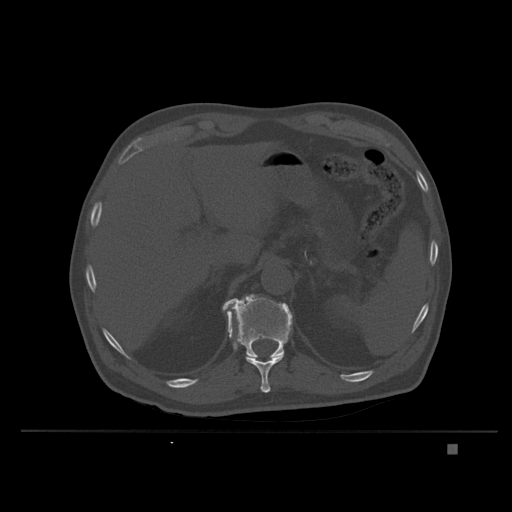
CT including the spine, one axial slice. Position 168 of 435 along the scan axis. Bone window (W 1800 / L 400 HU). 1.5 mm slice thickness. 512 × 512 image matrix. Male patient, age 73 years. From the clinical record (not read from this slice): primary cancer: skin.
Outlined on this slice (semi-automatically segmented with operator editing):
- T11 vertebra: box from (x=228, y=312) to (x=284, y=393) px
- T12 vertebra: (x=222, y=294)–(x=293, y=359)